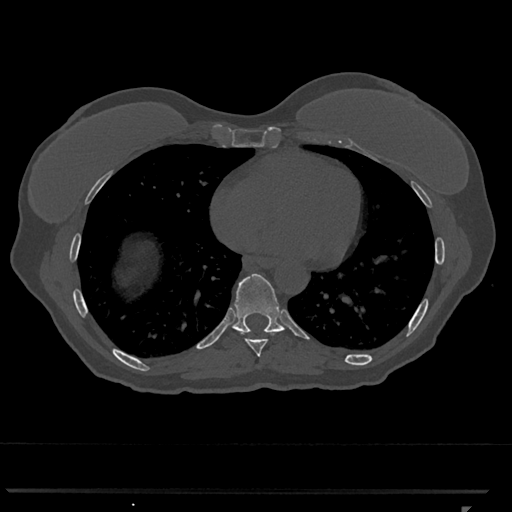
CT including the spine, one axial slice. Position 640 of 793 along the scan axis. Reconstruction kernel Br40s/3. 120 kVp. Bone window (W 1800 / L 400 HU). 0.5 mm slice thickness. 512 × 512 image matrix, field of view 380 × 380 mm. Female patient, age 62 years. From the clinical record (not read from this slice): primary cancer: renal.
Annotated regions visible in this slice (semi-automatic segmentation, software-assisted and operator-edited):
- T8 vertebra: bounding box <246,339,267,357> (left, top, right, bottom; pixels)
- T9 vertebra: <231,274,285,333>